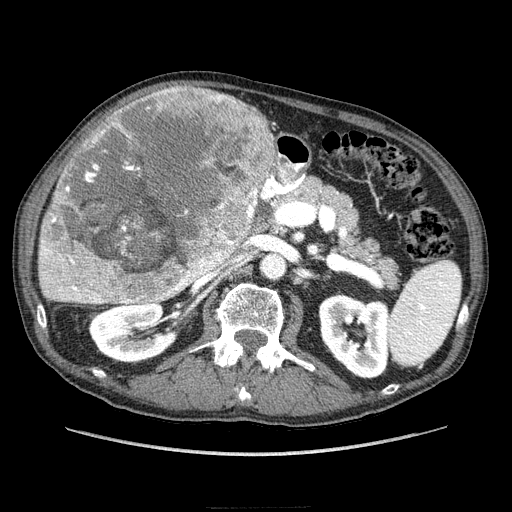
Contrast-enhanced abdominal CT (liver protocol), one axial slice; position 121 of 218 along the scan axis; reconstruction kernel STANDARD; 100 kVp; soft-tissue window (W 400 / L 40 HU); 2.5 mm slice thickness; 512 × 512 image matrix, field of view 380 × 380 mm. Case-level facts recorded for this patient, not image findings: diagnosis: hepatocellular carcinoma (patient treated with transarterial chemoembolisation; whether this scan precedes or follows treatment is not stated here); TNM stage (as recorded): Stage-IIIA; Child-Pugh class: A; tumour nodularity: multinodular; tumour size: 20 cm.
Annotated regions visible in this slice (semi-automatic segmentation, software-assisted and operator-edited):
- liver parenchyma outside the tumour (the mass and vessels are separate outlines, so this box may not span the whole liver): bounding box (x1, y1, x2, y2) in pixels: (38, 90, 285, 304)
- mass: (43, 81, 276, 305)
- liver vessels: (60, 286, 81, 299)